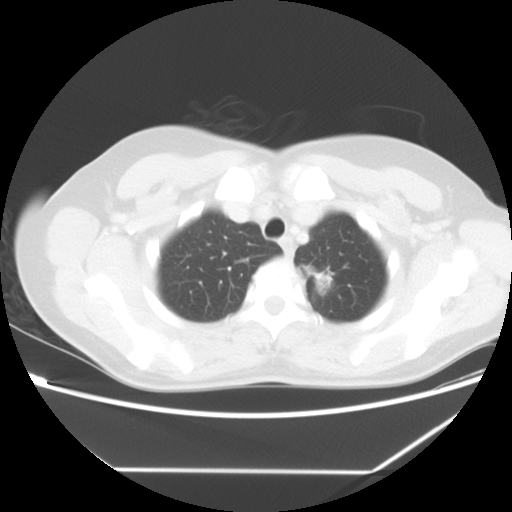
Chest CT, one axial slice. Position 50 of 60 along the scan axis. Reconstruction kernel STANDARD. Lung window (W 1500 / L -600 HU). 512 × 512 image matrix. Patient: female, 43 years. Case-level facts recorded for this patient, not image findings: clinical TNM (as recorded): T1c N0 M1b.
Outlined on this slice (rectangle marked by the reading radiologist):
- lung tumour (recorded histology: adenocarcinoma): box from (x=304, y=261) to (x=337, y=303) px